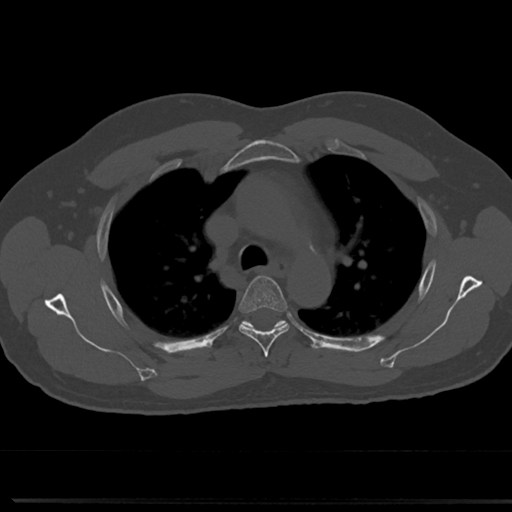
CT including the spine, one axial slice. Slice 535 of 817 in the series (ordered by position). Reconstruction kernel Br40s/3. 120 kVp. Bone window (W 1800 / L 400 HU). 512 × 512 image matrix. Male patient, age 61 years. From the clinical record (not read from this slice): primary cancer: prostate.
Annotated regions visible in this slice (semi-automatically segmented with operator editing):
- T4 vertebra: bounding box (x1, y1, x2, y2) in pixels: (238, 275, 290, 355)
- T5 vertebra: (245, 321, 283, 326)